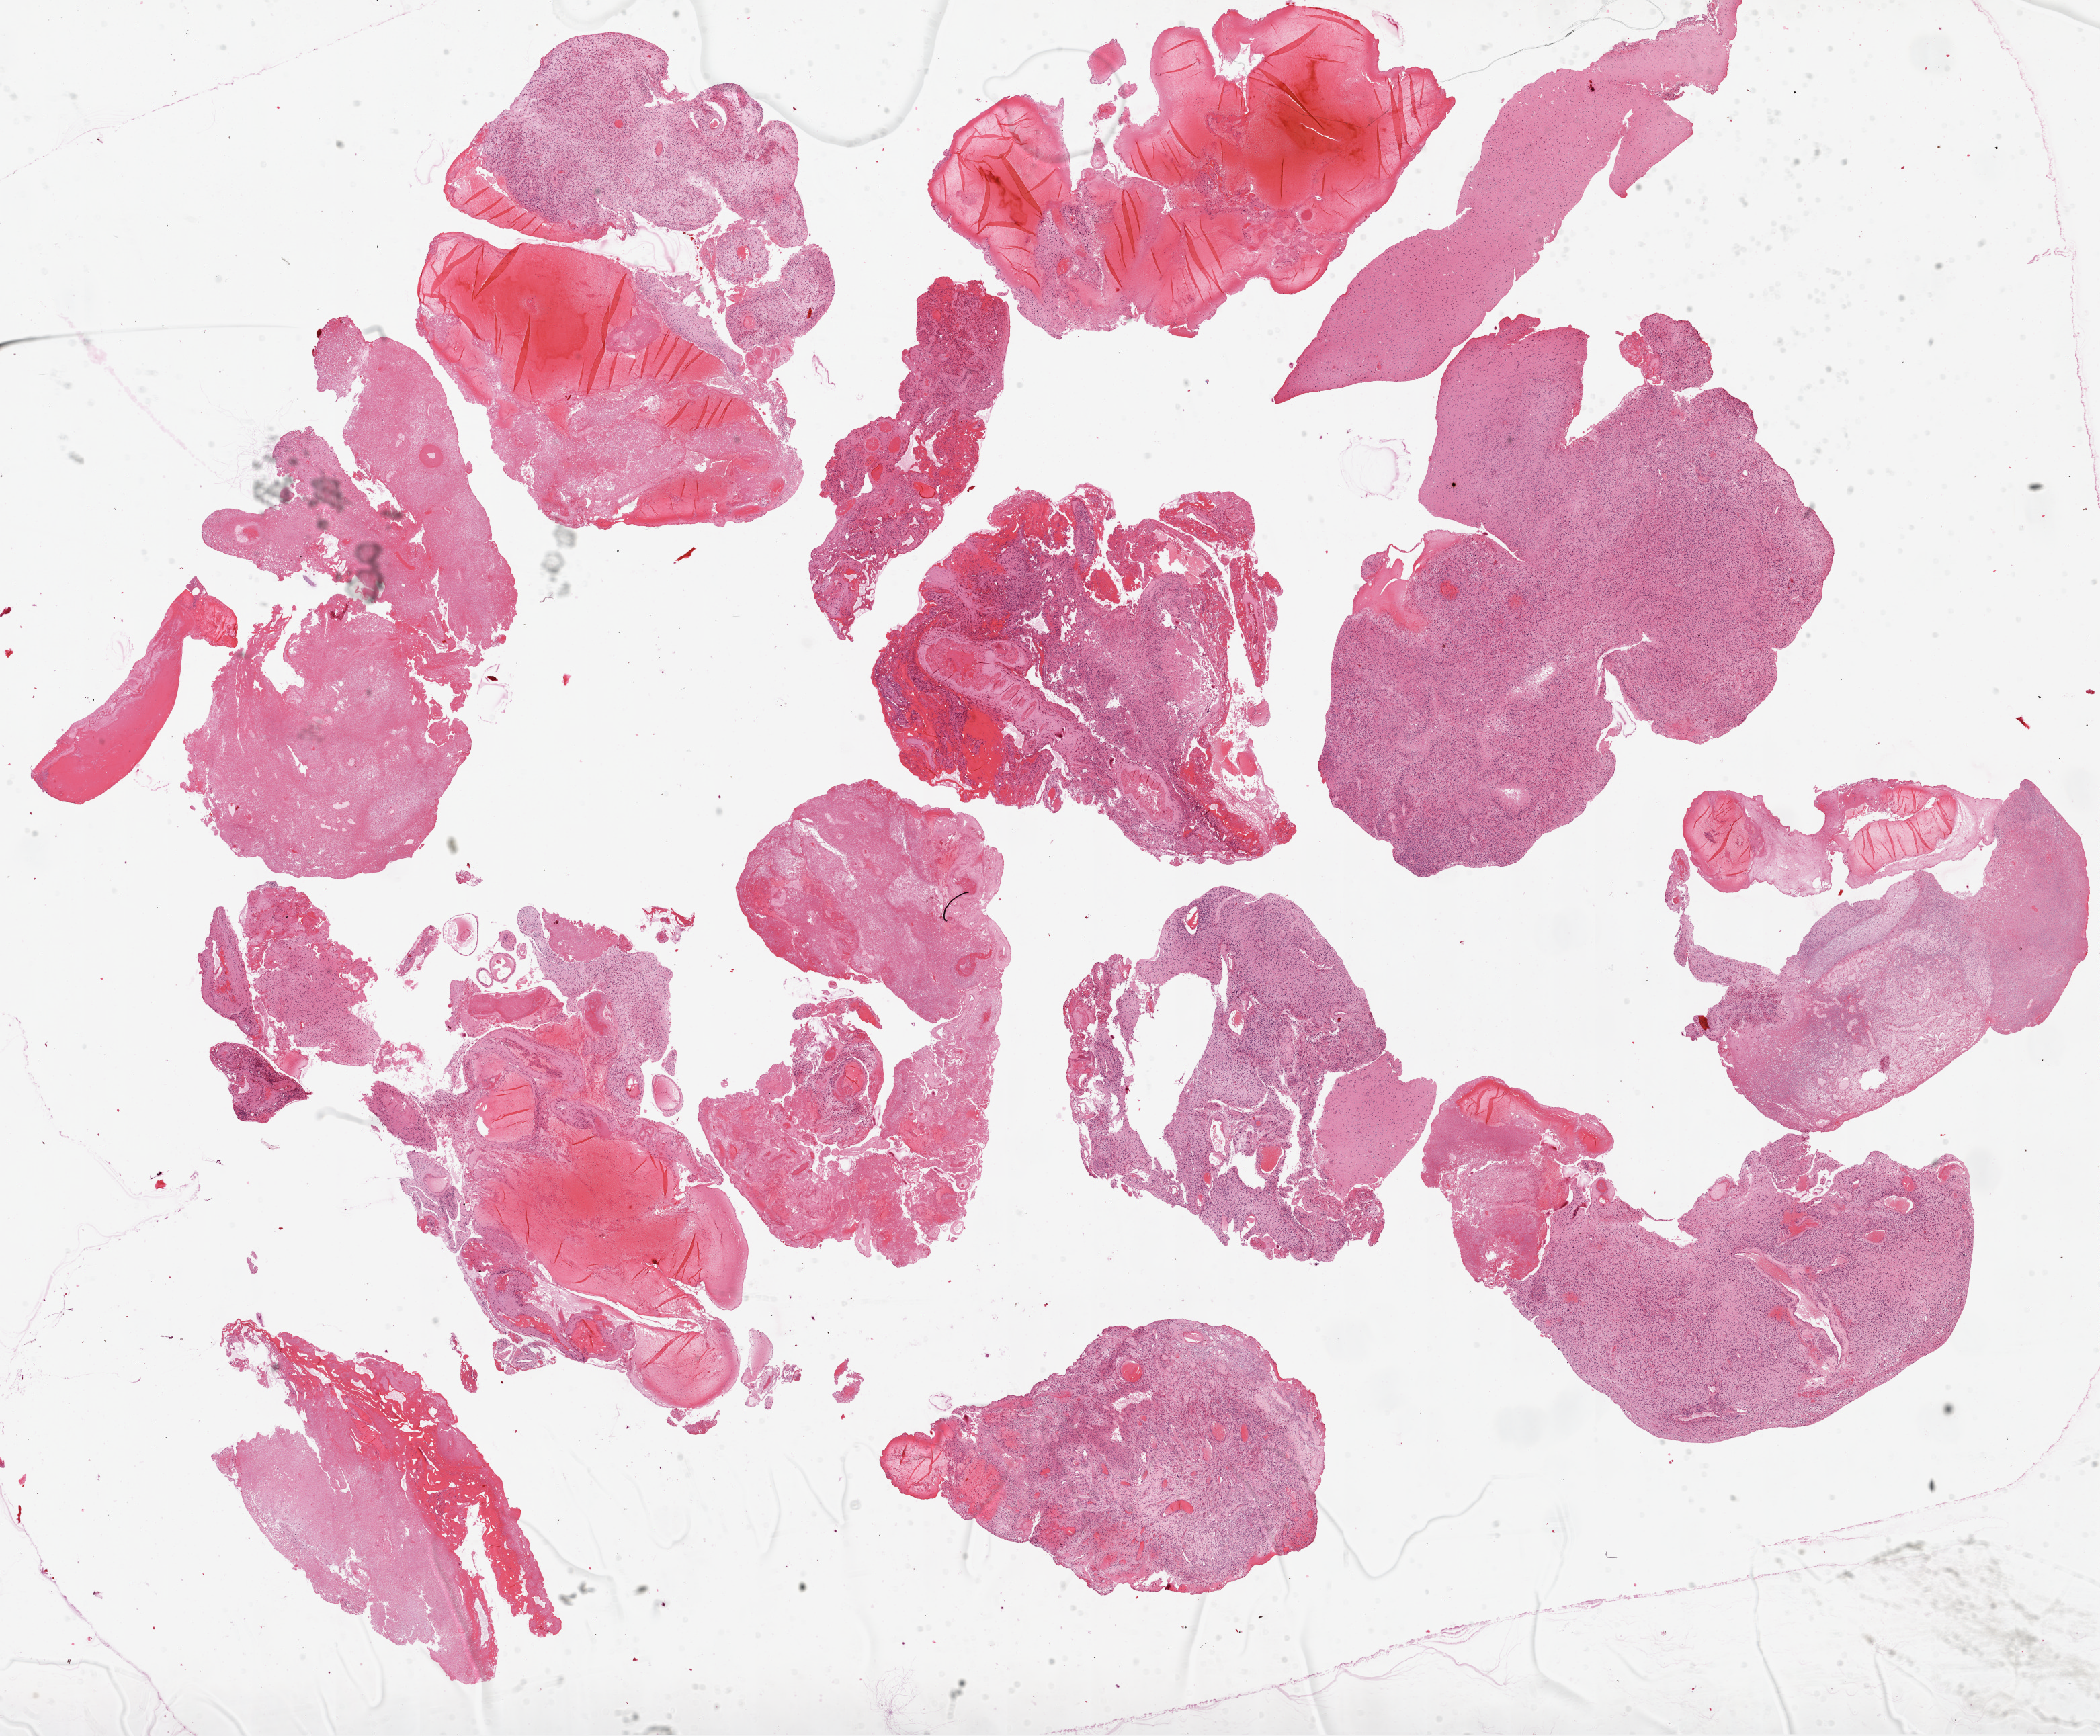
Digitized H&E tissue section (whole slide) — a low-resolution overview of the entire scanned area, about 25.1 x 20.7 mm, FFPE section, brain, primary tumour sample. Patient: male, age at initial diagnosis 57 years.
• pathologic diagnosis: Glioblastoma